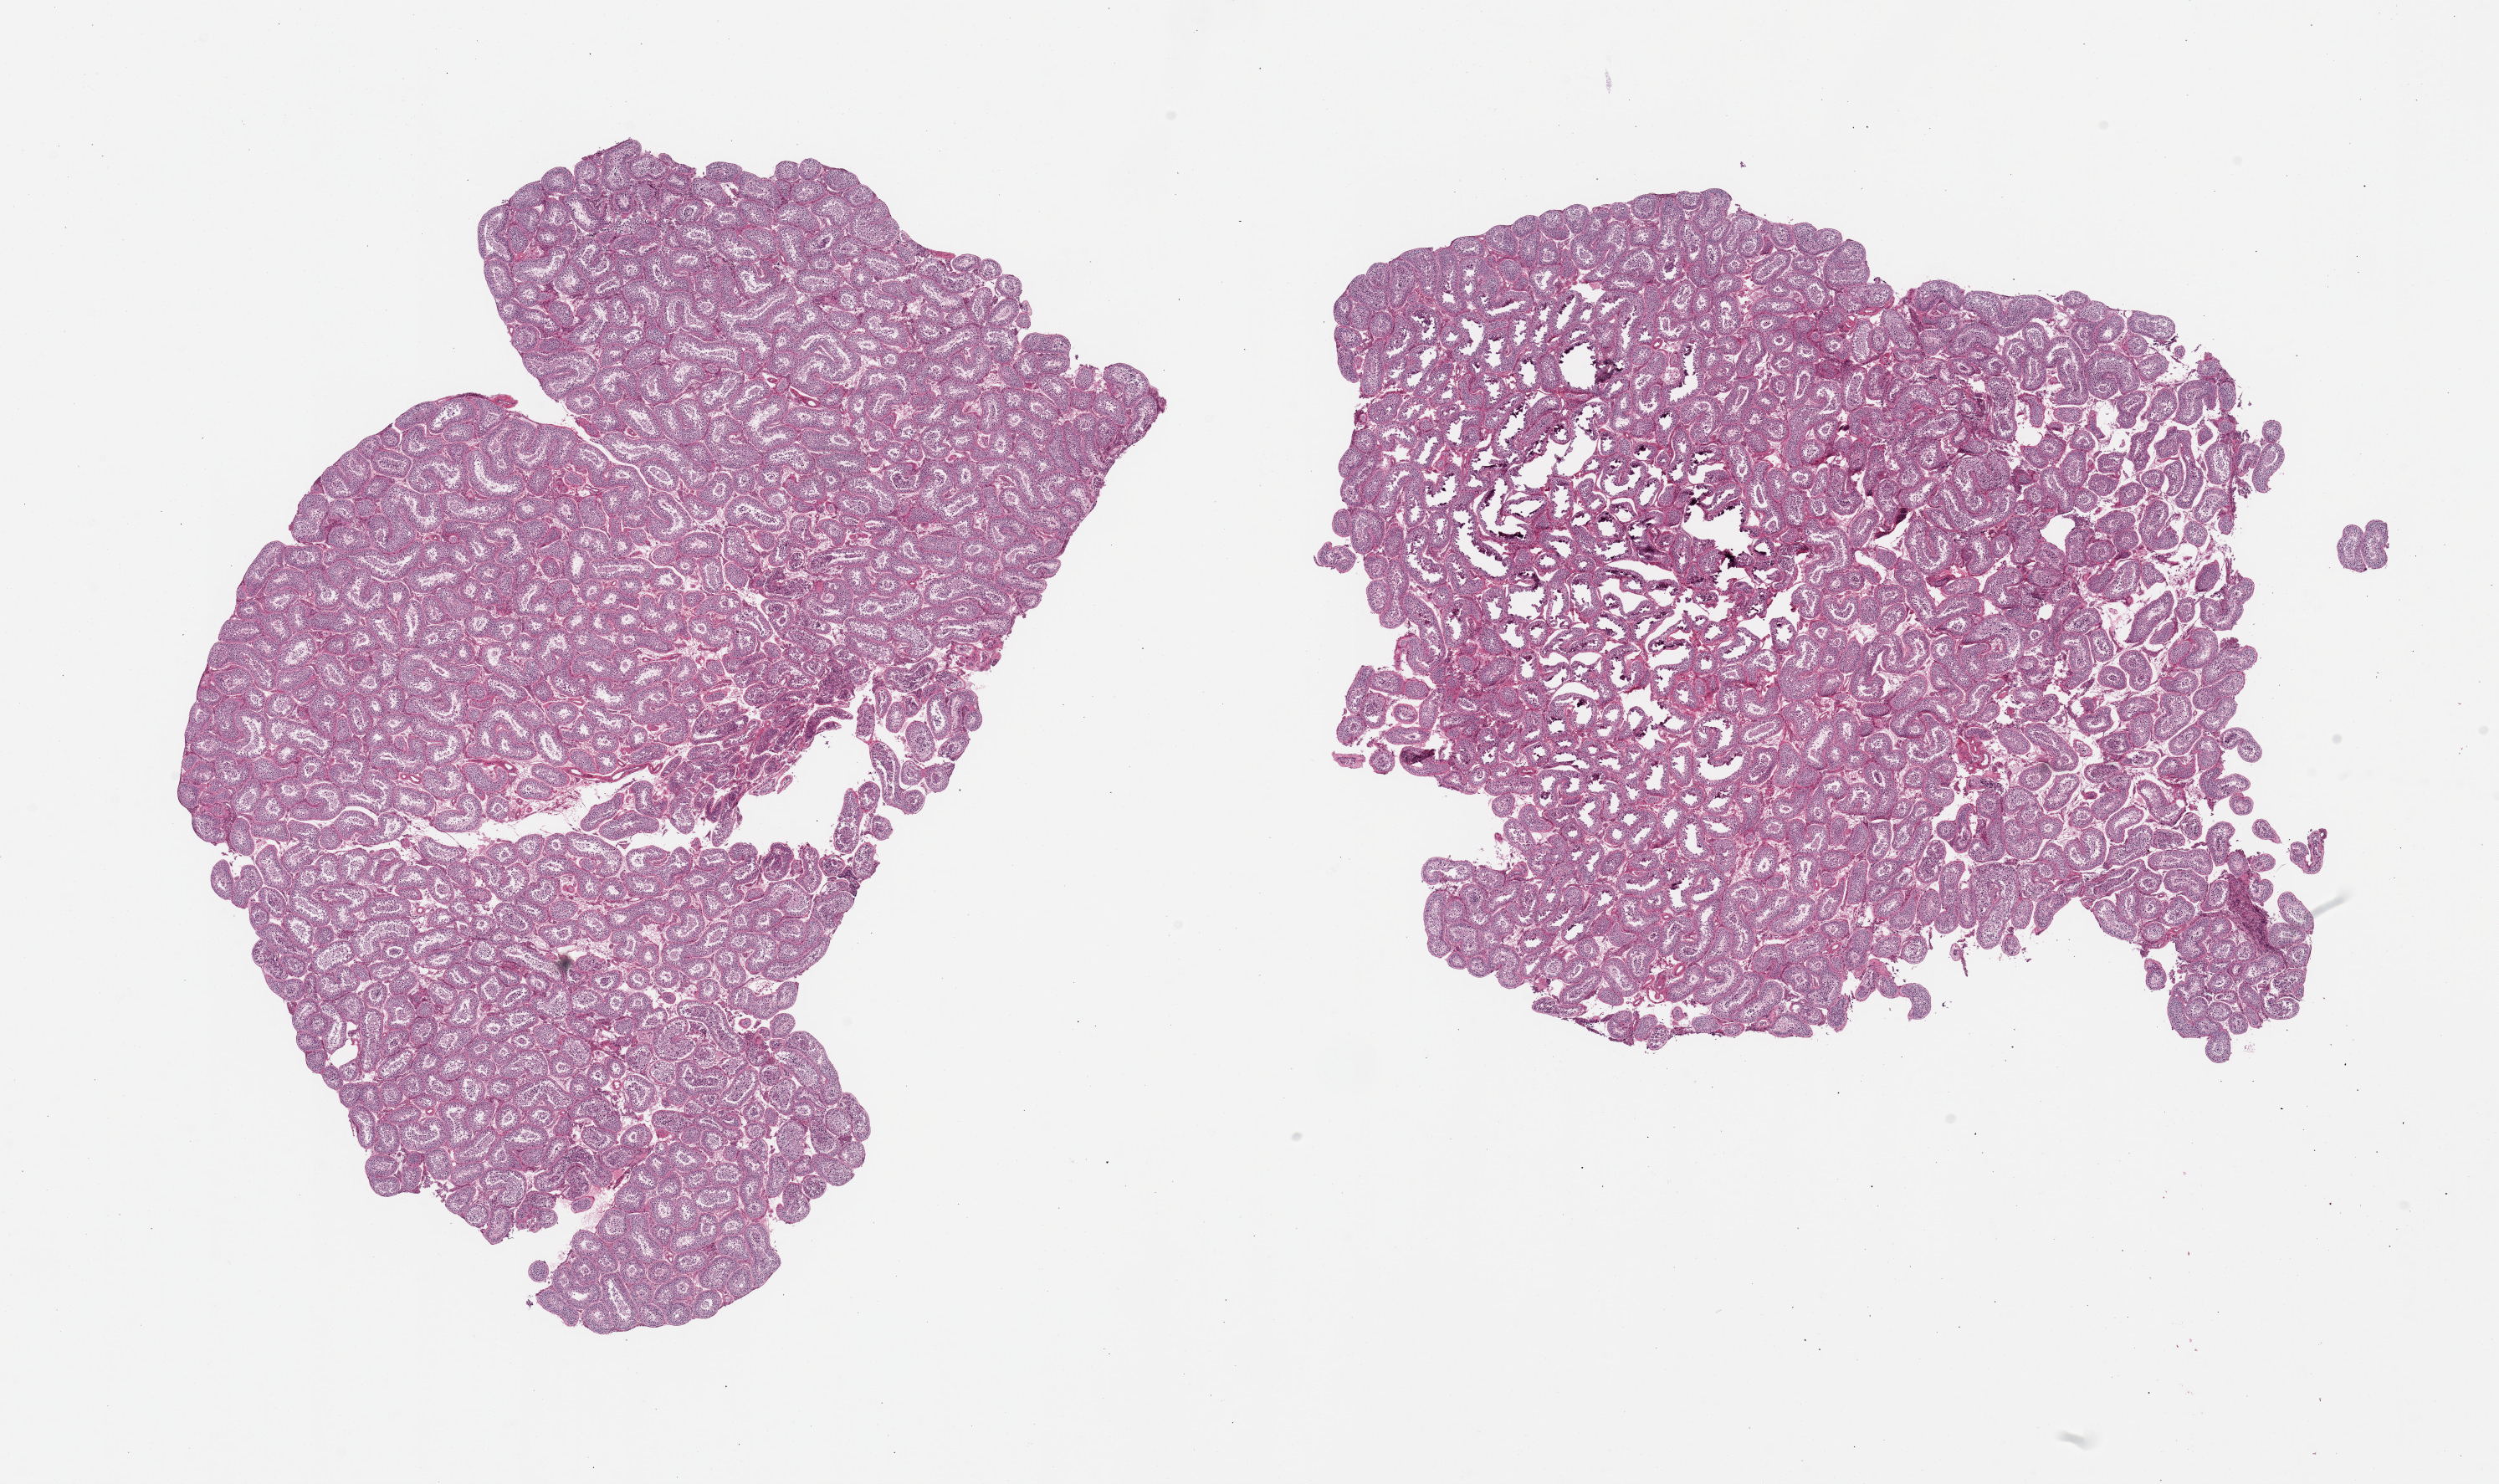
H&E whole-slide image, low-resolution overview of the scanned area, about 23.6 x 14.0 mm; PAXgene-fixed, paraffin-embedded tissue; section of testis (target tissue); tissue donor sample. Male donor.
* review note (as recorded): 2 pieces; active spermatogenesis